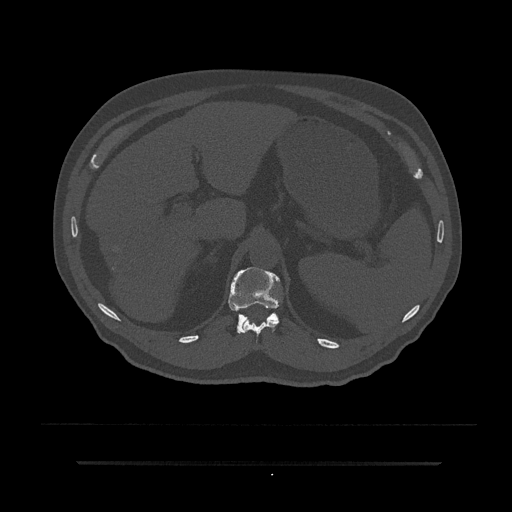
CT including the spine, one axial slice; position 238 of 797 along the scan axis; bone window (W 1800 / L 400 HU); 512 × 512 image matrix, field of view 464 × 464 mm. Patient: male, 59 years. From the clinical record (not read from this slice): primary cancer: bile ducts; vertebrae with lytic lesions (as recorded): T10.
Structures marked on this image (semi-automatically segmented with operator editing):
- T11 vertebra: bounding box [x1, y1, x2, y2] px = [242, 319, 279, 343]
- T12 vertebra: [228, 267, 280, 333]